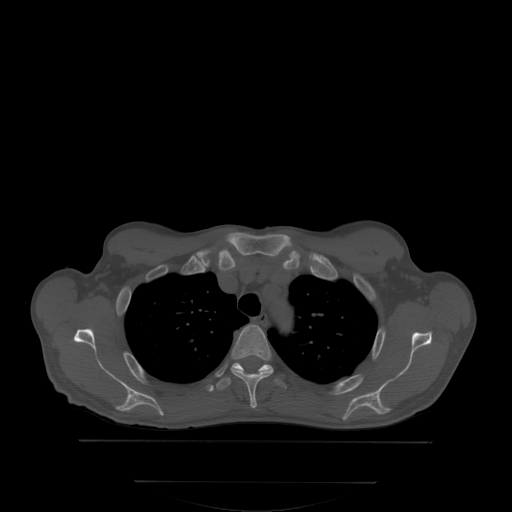
CT including the spine, one axial slice. Slice 265 of 350 in the series (ordered by position). Bone window (W 1800 / L 400 HU). 2.5 mm slice thickness. 512 × 512 image matrix, field of view 500 × 500 mm. Patient: male, 58 years. From the clinical record (not read from this slice): primary cancer: prostate.
Annotated regions visible in this slice (semi-automatically segmented with operator editing):
- T3 vertebra: bounding box <232,324,272,407> (left, top, right, bottom; pixels)
- T4 vertebra: <216,363,279,389>